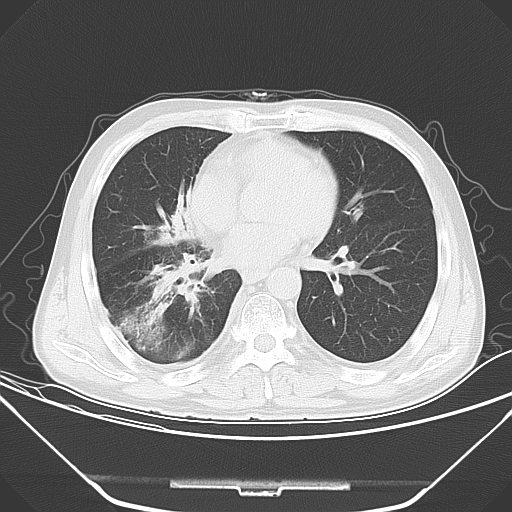
Chest CT, one axial slice; position 21 of 52 along the scan axis; 120 kVp; lung window (W 1500 / L -600 HU); 512 × 512 image matrix, field of view 379 × 379 mm. Patient: male, 54 years. Case-level facts recorded for this patient, not image findings: clinical TNM (as recorded): T2 N1 M0; histopathological grade: G3.
Outlined on this slice (rectangle marked by the reading radiologist):
- lung tumour (recorded histology: adenocarcinoma): box from (x=119, y=299) to (x=166, y=353) px